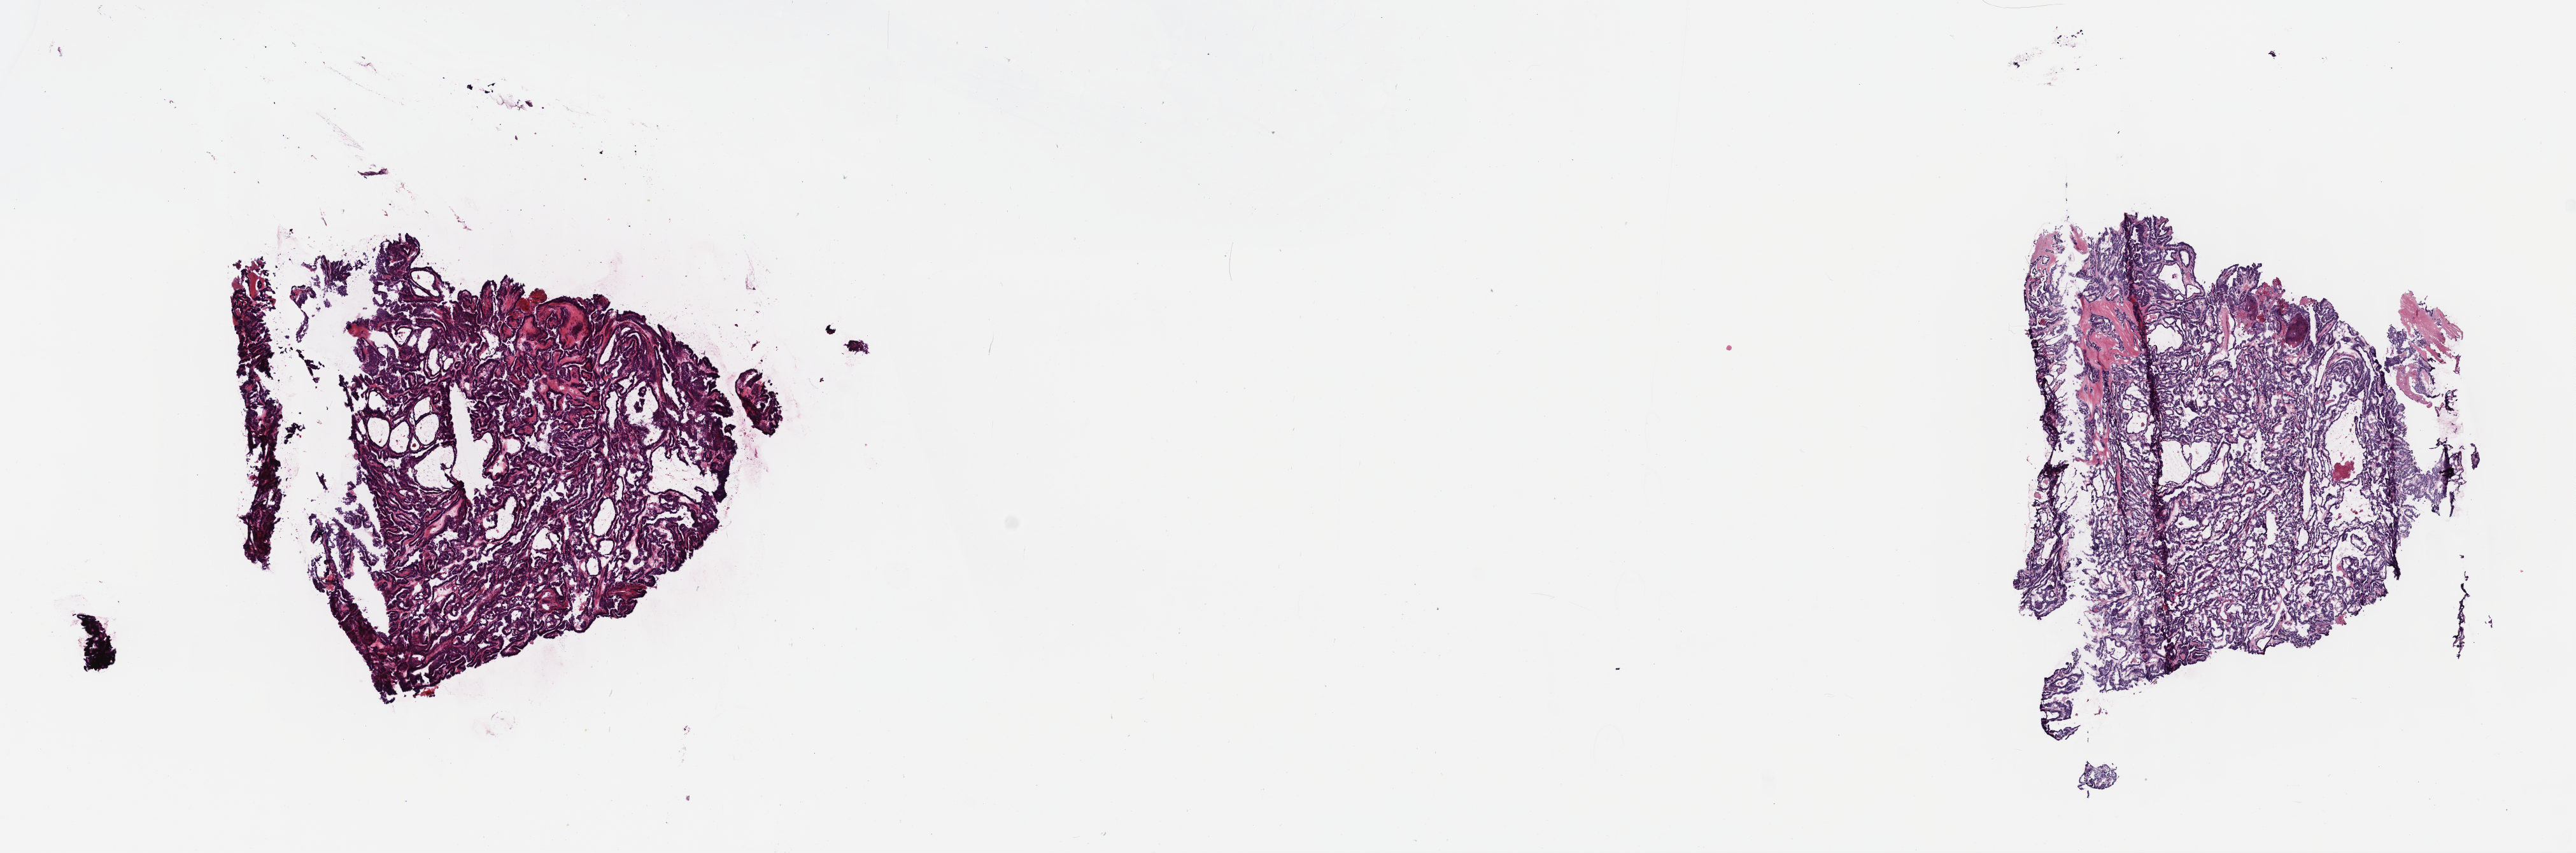
H&E whole-slide image, low-resolution overview of the scanned area, about 15.9 x 5.3 mm, frozen section from the top of the tissue portion, sample: primary tumour, thyroid. Female, age 34 years at initial diagnosis. Pathologist review of this section (percent, as recorded): tumour cells 90%, tumour nuclei 100%, normal cells 0%, stromal cells 10%, necrosis 0%. Inflammatory infiltration, as recorded: lymphocyte infiltration 0%, monocyte infiltration 1%, neutrophil infiltration 0%.
• TNM: T2 N1 M0
• diagnosis: Papillary adenocarcinoma, NOS (thyroid gland)
• AJCC pathologic stage: I
• lymph nodes positive (case pathology): 4 of 7 examined